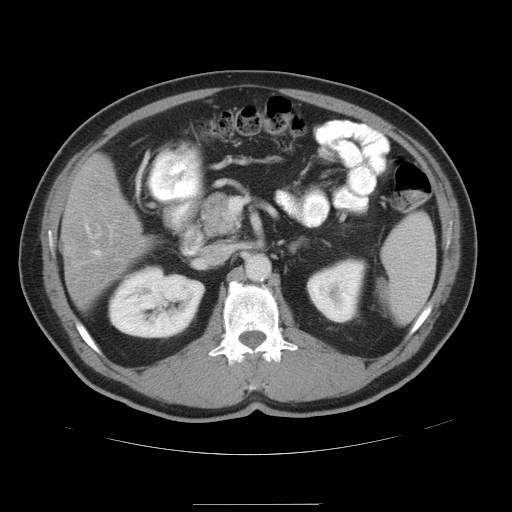
Contrast-enhanced abdominal CT, one axial slice; slice 23 of 47 in the series (ordered by position); 120 kVp; intravenous contrast given; soft-tissue window (W 400 / L 40 HU); 5 mm slice thickness; 512 × 512 image matrix, field of view 420 × 420 mm. Male patient, age 61 years. From the clinical record (not read from this slice): diagnosis: colorectal cancer liver metastases, imaged before liver resection; multiple liver metastases: no; largest metastasis: 1.2 cm; disease in both lobes: no.
Annotated regions visible in this slice (manually delineated by an expert):
- hepatic veins: bounding box [x1, y1, x2, y2] px = [94, 250, 101, 254]
- liver: [63, 155, 147, 309]
- planned liver remnant (the part of the liver to remain after resection): [67, 155, 147, 271]
- liver metastasis: [61, 240, 77, 253]